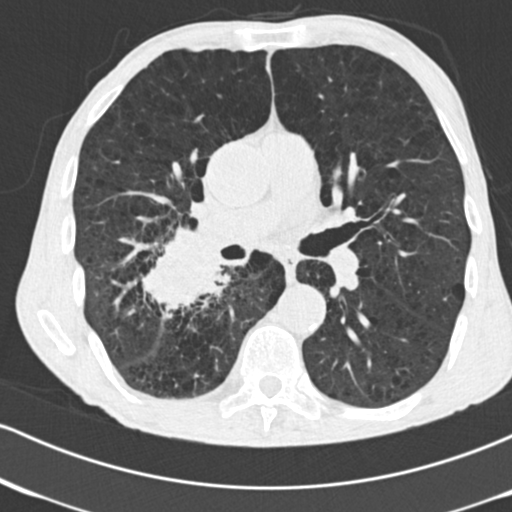
Axial slice from a low-dose chest CT screening exam, second annual screen, lung window (W 1500 / L -600 HU), 2 mm slice thickness. Male participant, aged 64 years at enrolment. Current smoker at enrolment.
• Lesion marked by an expert reader, bounding box <132,230,239,328> (left, top, right, bottom; pixels).
• Screening reader's record for this exam (one nodule recorded; not confirmed to be the boxed lesion): non-calcified nodule or mass ≥4 mm, 52 × 37 mm, spiculated (stellate) margins, soft tissue attenuation, pre-existing on the prior screen: no.
• Official screen result: positive, other.
• Lung cancer was diagnosed 28 days after this screen: adenocarcinoma, NOS, right lower lobe, stage IV (AJCC 6th edition), 60 mm at pathology.